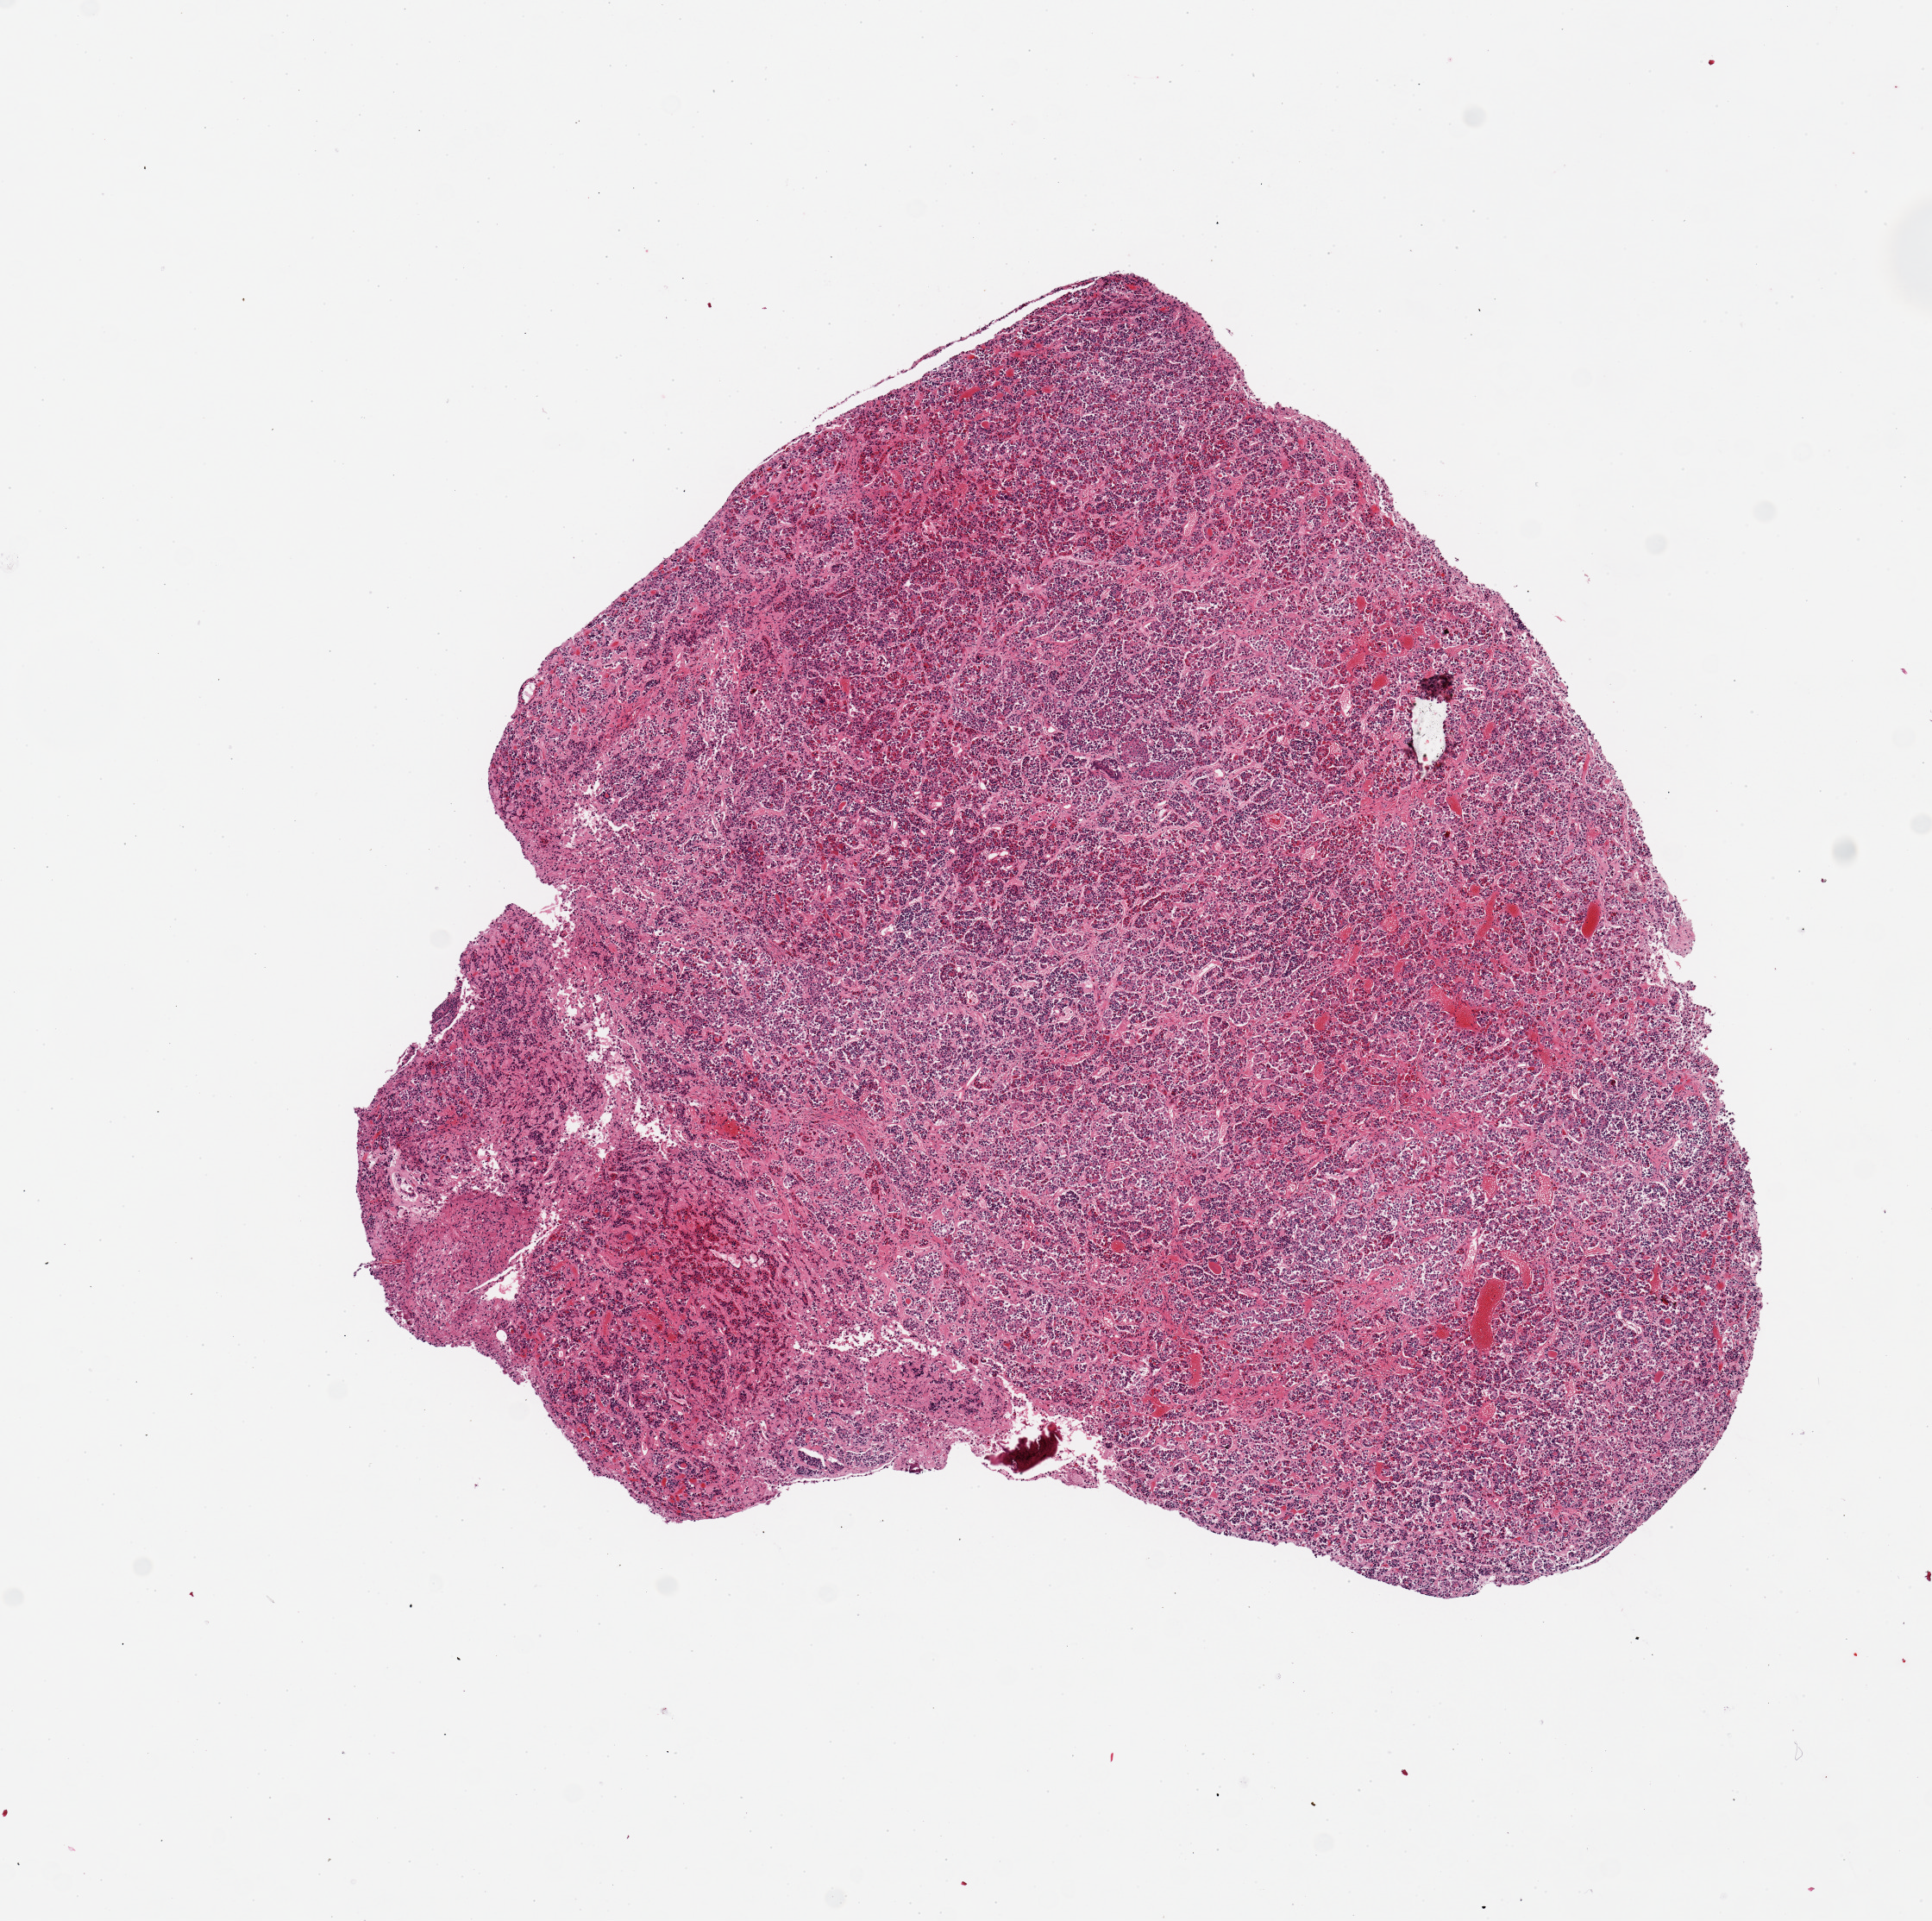
Whole-slide image, haematoxylin and eosin stain — whole scanned area (about 8.9 x 8.8 mm) shown as a low-resolution overview; PAXgene-fixed paraffin-embedded (PFPE) section; target tissue: pituitary; tissue donor sample. Donor: male.
* pathologist's review note for this sample: 1 piece approaching score 2, all adenohypophysis